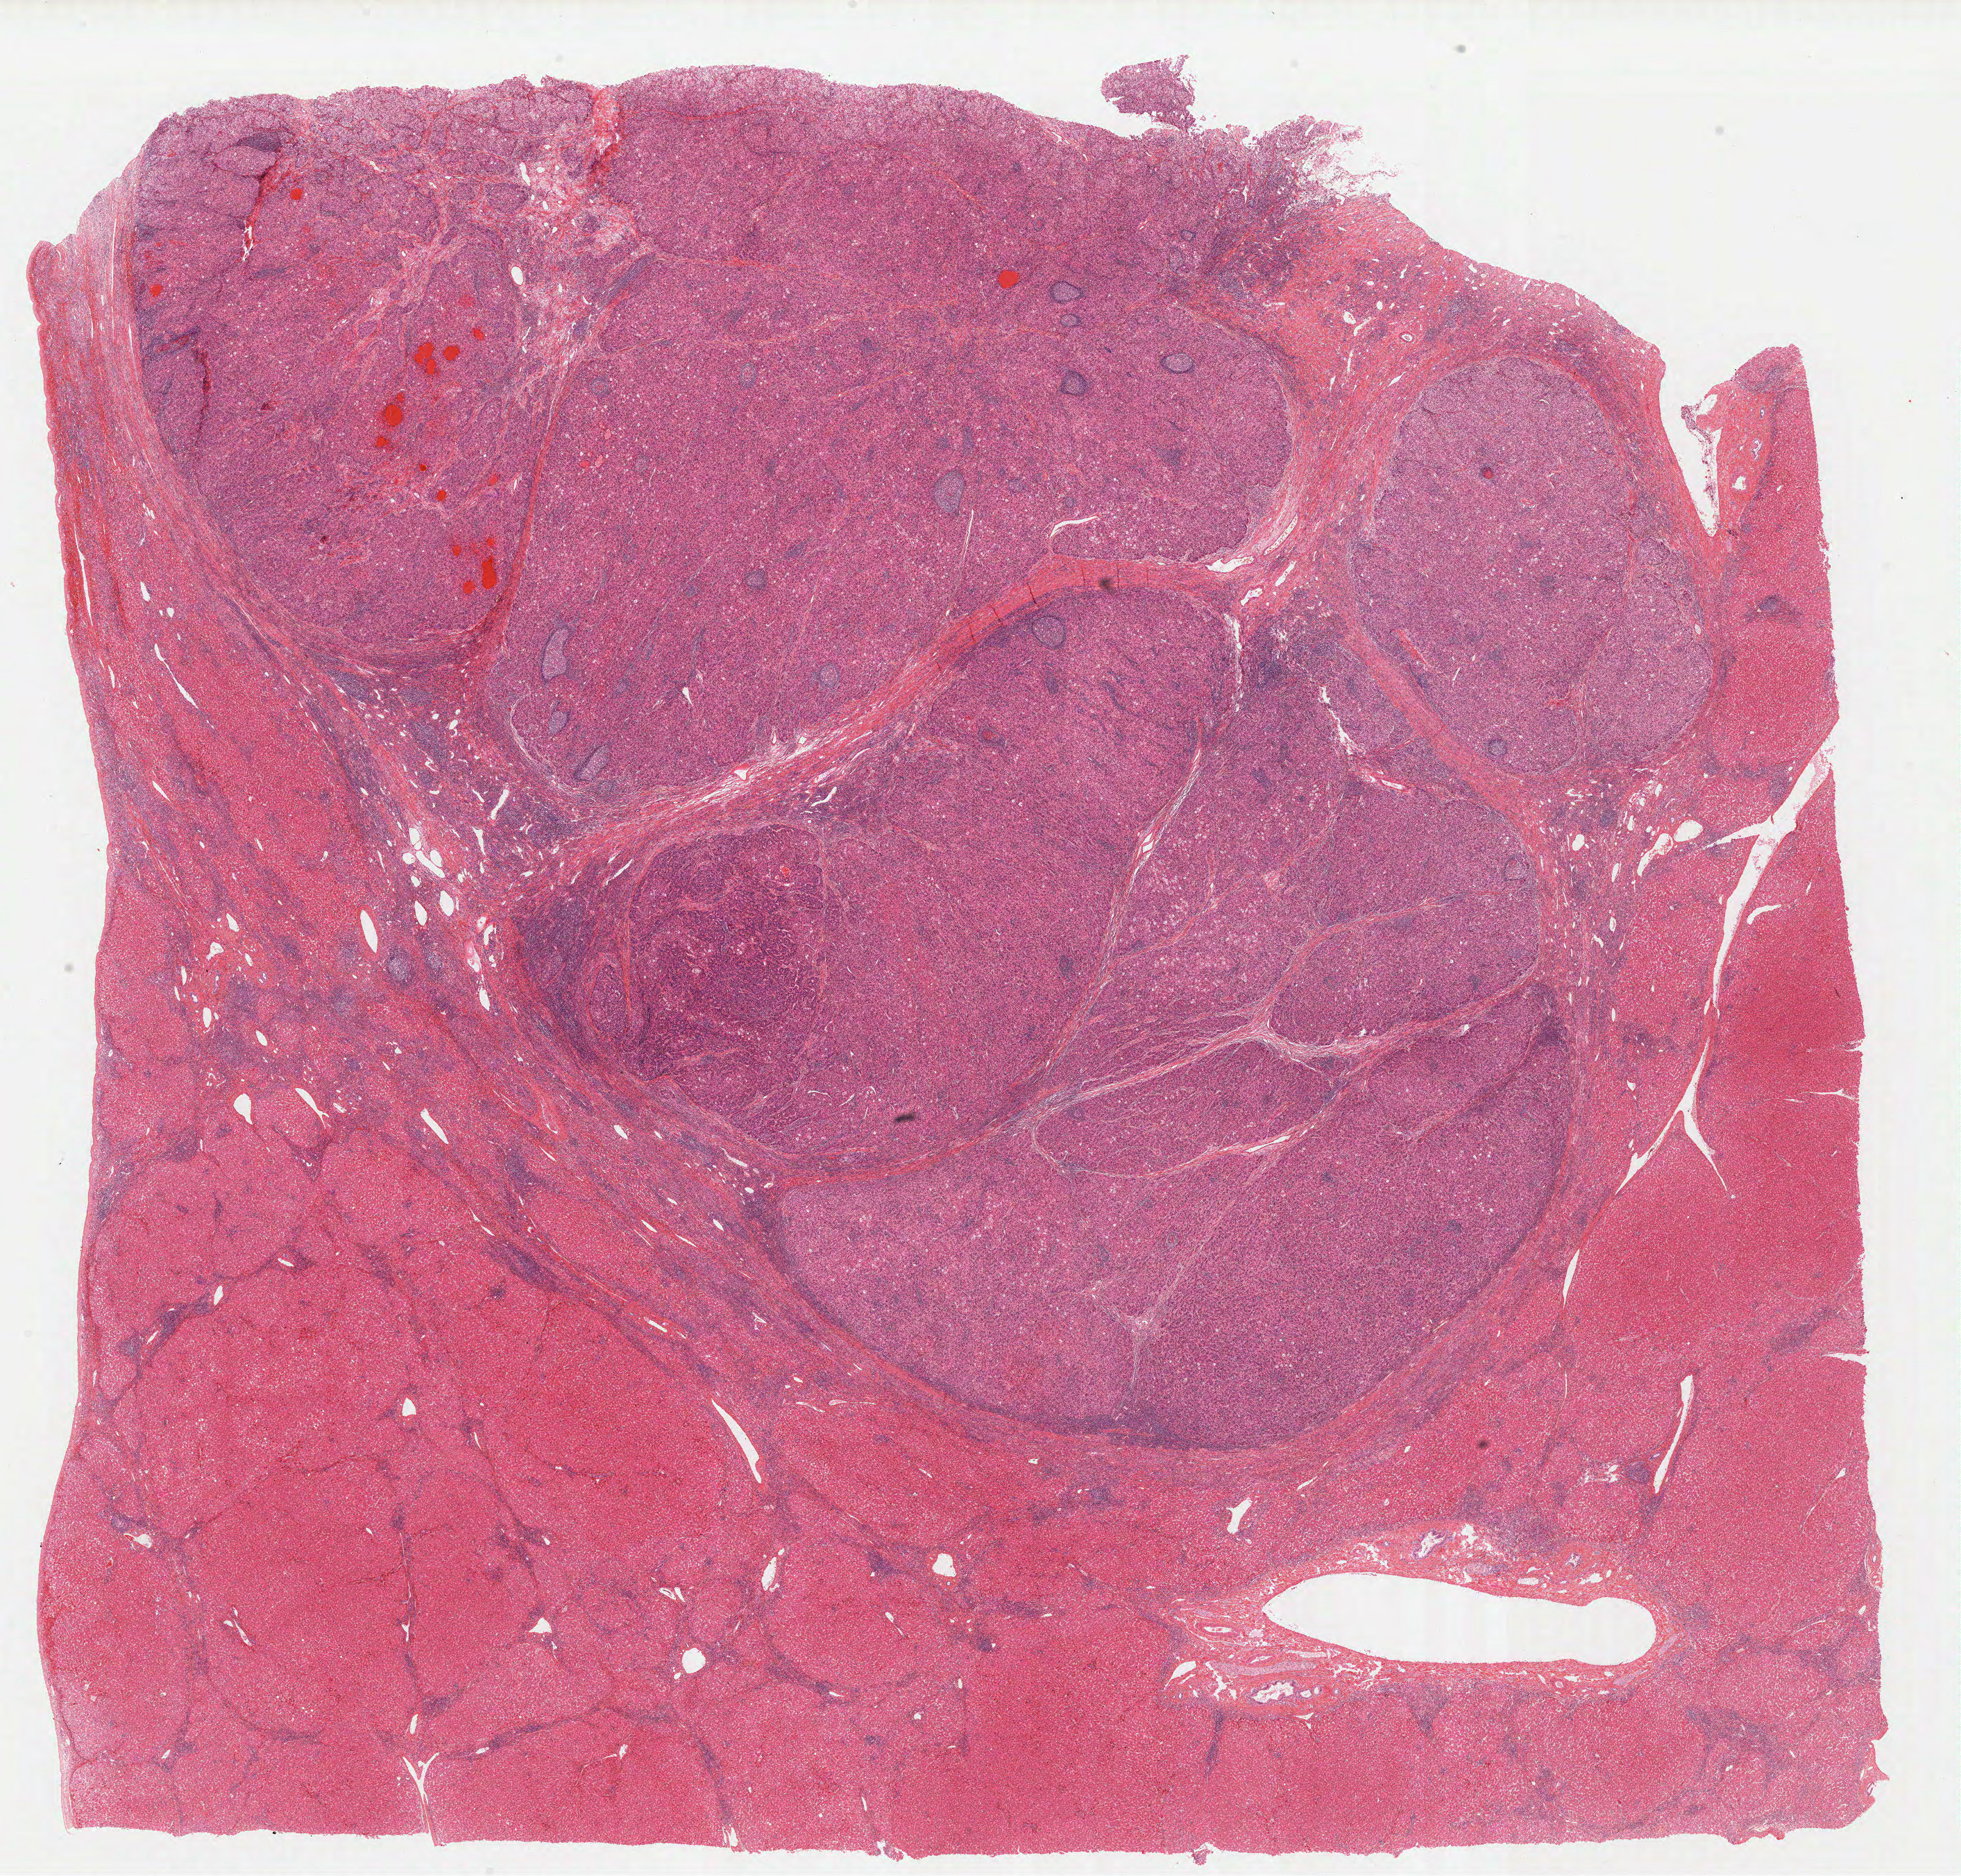
H&E whole-slide image, shown as a low-resolution overview of the whole scanned area (about 22.3 x 21.4 mm, from a 40x scan), formalin-fixed paraffin-embedded (FFPE) diagnostic section, primary tumour sample from the liver. Patient: male, age at initial diagnosis 38 years.
Histologic diagnosis: Hepatocellular carcinoma, NOS.